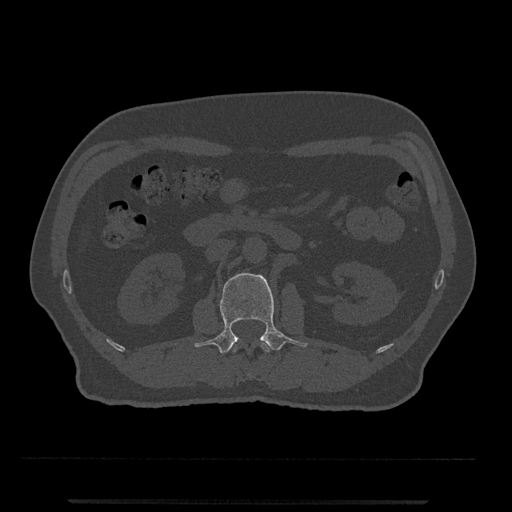
CT including the spine, one axial slice. Slice 280 of 797 in the series (ordered by position). 120 kVp. Bone window (W 1800 / L 400 HU). 0.5 mm slice thickness. 512 × 512 image matrix, field of view 419 × 419 mm. Male patient, age 63 years. From the clinical record (not read from this slice): primary cancer: prostate.
Annotated regions visible in this slice (semi-automatic segmentation, software-assisted and operator-edited):
- L1 vertebra: box from (x=230, y=341) to (x=270, y=354) px
- L2 vertebra: (x=194, y=273)–(x=307, y=354)